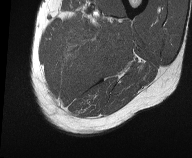
MRI of an extremity soft-tissue mass, one axial slice. Position 10 of 61 along the scan axis. MR volume resampled by the dataset authors to the PET/CT grid (not the native acquisition matrix). 3.27 mm slice thickness. 192 × 158 image matrix. Male patient. Case-level facts recorded for this patient, not image findings: histological type: pleiomorphic liposarcoma; grade: high; site of the primary tumour: left thigh.
Outlined on this slice (expert contour drawn on MRI and transferred to this co-registered scan by the dataset authors):
- gross tumour volume including surrounding oedema: bounding box (x1, y1, x2, y2) in pixels: (68, 14, 112, 45)